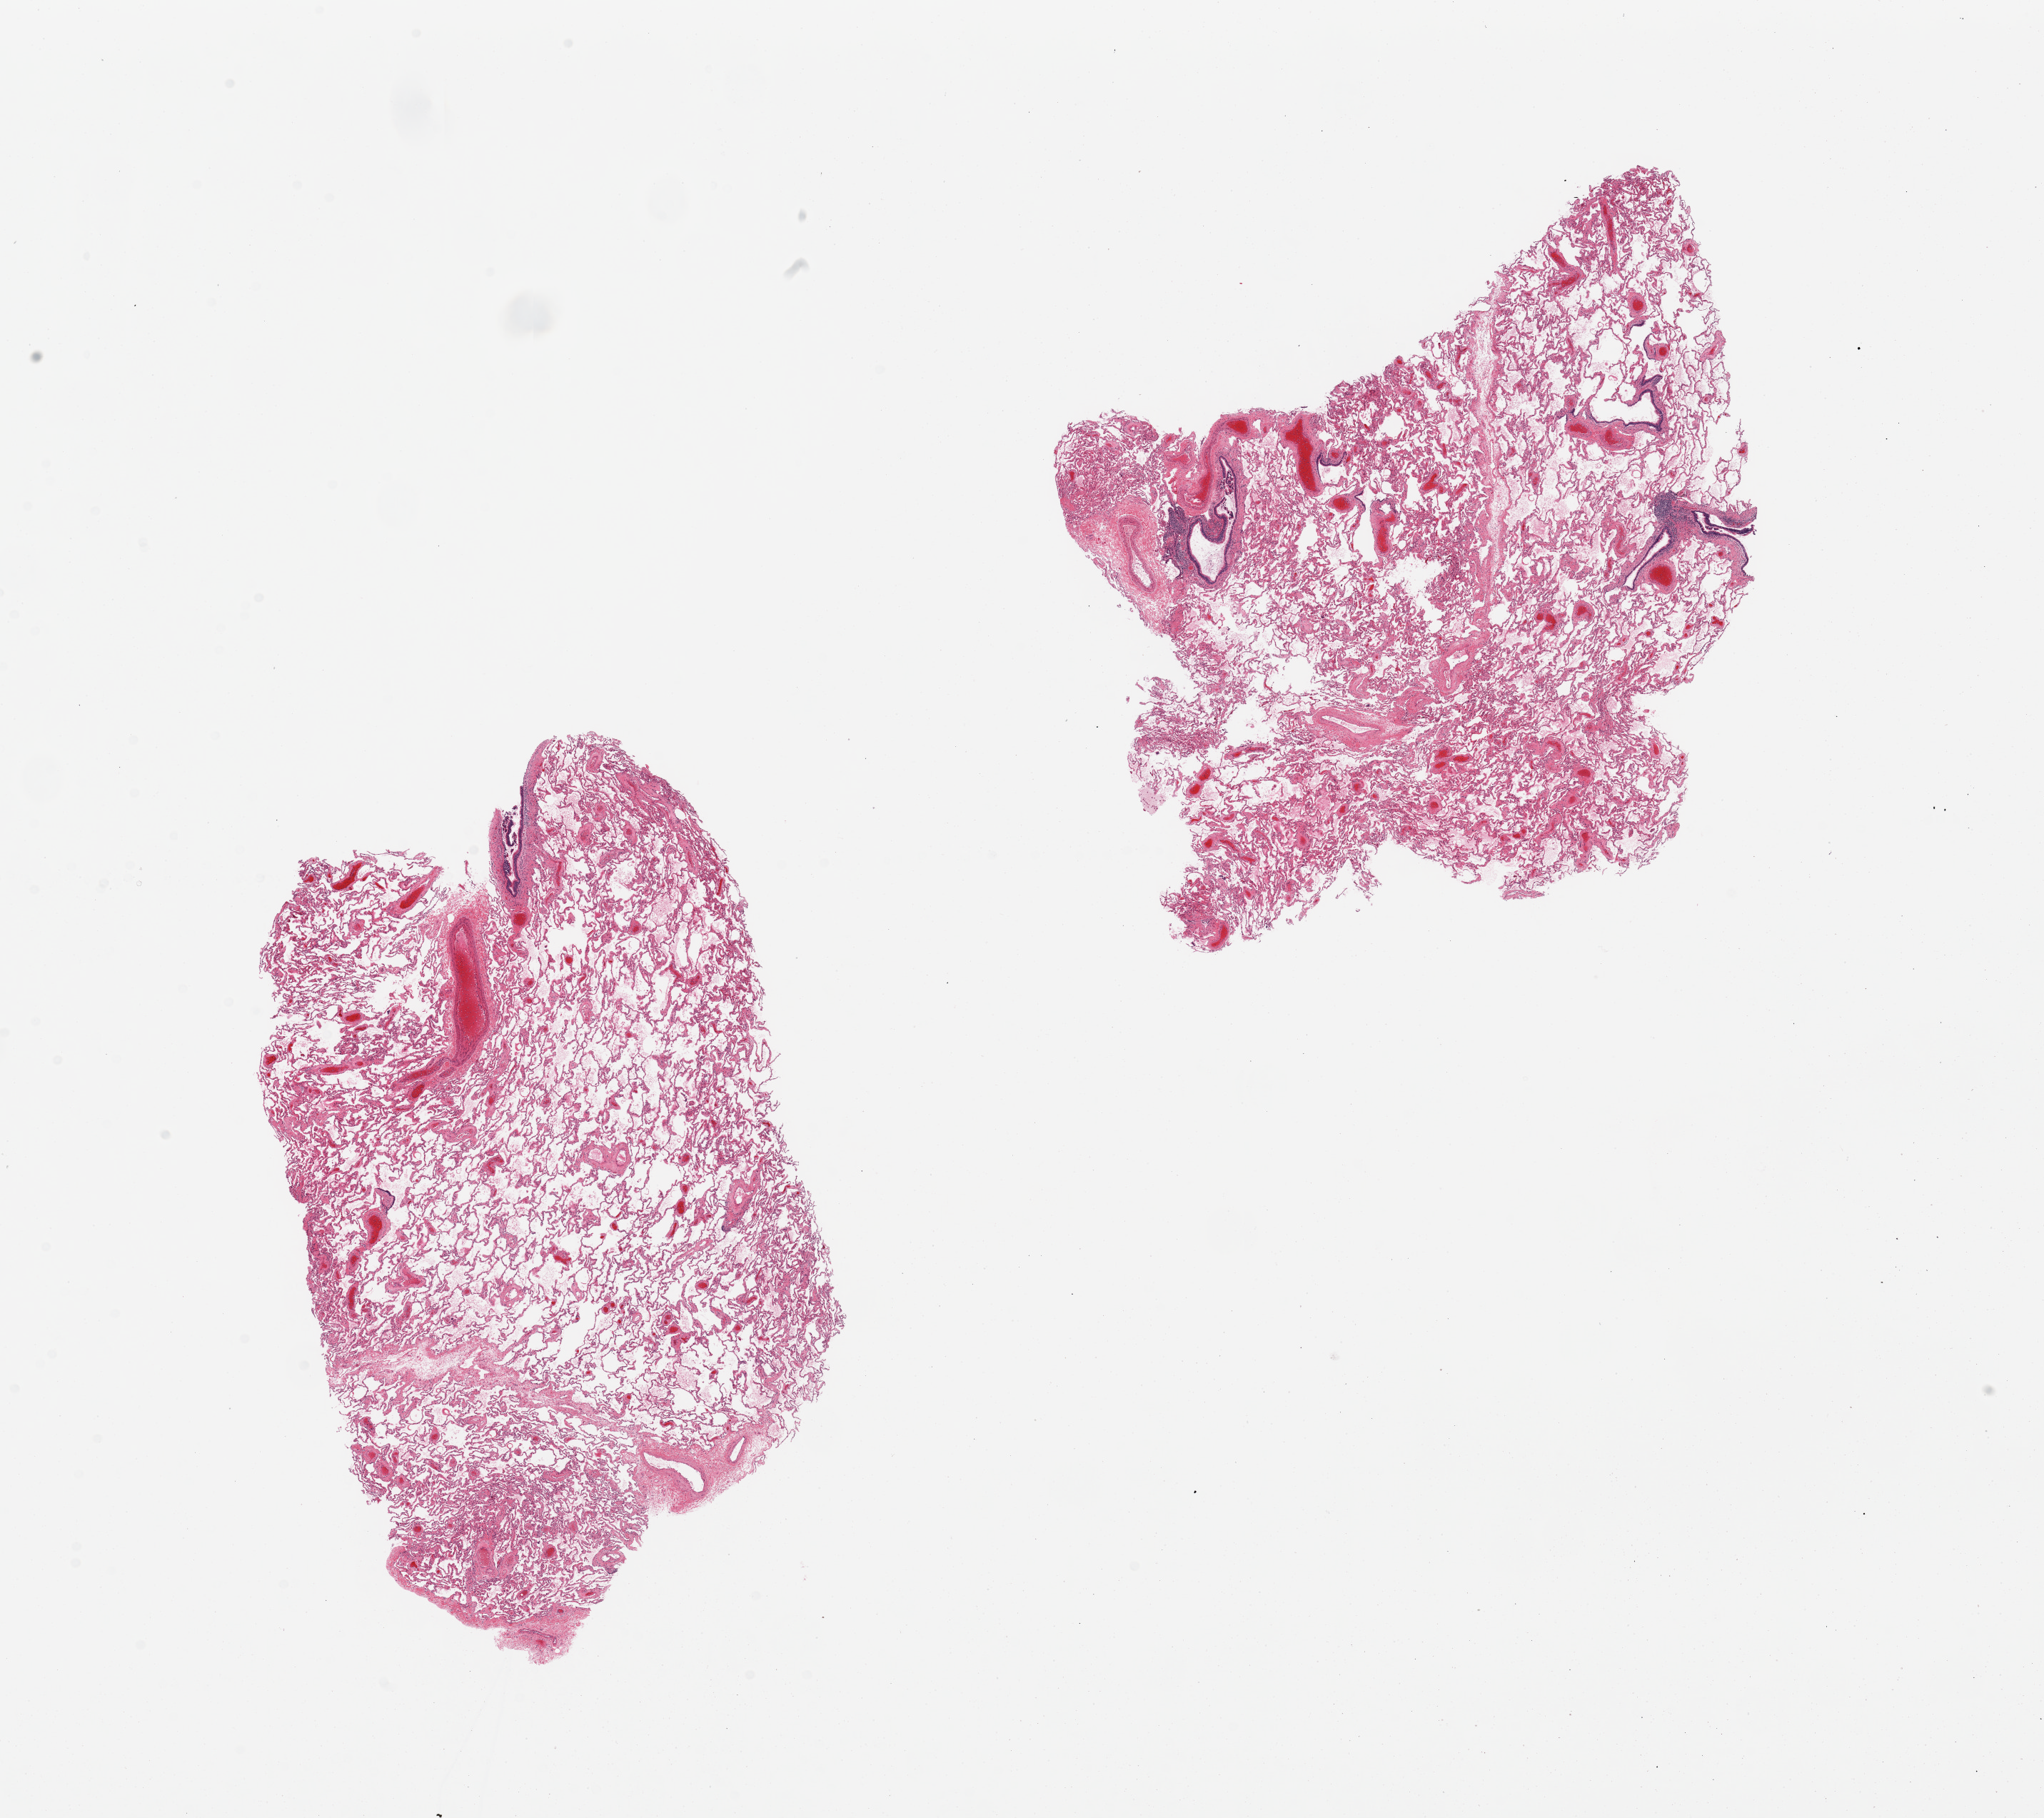
Whole-slide image, H&E stain, shown as a low-resolution overview of the whole scanned area (about 22.6 x 20.1 mm, slide scanned at 20x). PAXgene-fixed paraffin-embedded (PFPE) section. Target tissue: lung. Donor tissue sample. Donor: female.
• pathologist's review note for this sample: 2 pieces, mild congestion, prominent vascular congestion